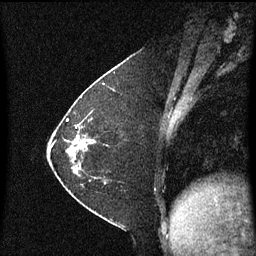
Breast MRI (dynamic contrast-enhanced), one sagittal slice. Slice 23 of 60 in the series (ordered by position). Dynamic contrast-enhanced series, image 2 of 3 at this slice position (ordered by acquisition). 1.5 T. TE 4.2 ms, TR 8.4 ms. 256 × 256 image matrix, field of view 200 × 200 mm. Patient: female, 36 years. Case-level facts recorded for this patient, not image findings: setting: breast cancer imaged before/during neoadjuvant chemotherapy; receptor status: HR-positive, HER2-negative.
Outlined on this slice (semi-automatic segmentation, software-assisted and operator-edited):
- analysis volume of interest (the breast-tissue region the enhancement analysis was run in; not a lesion): box from (x=72, y=116) to (x=107, y=187) px
- tumour enhancement mask (voxels above the 70 % enhancement threshold inside the analysis volume of interest): (x=72, y=138)–(x=91, y=171)